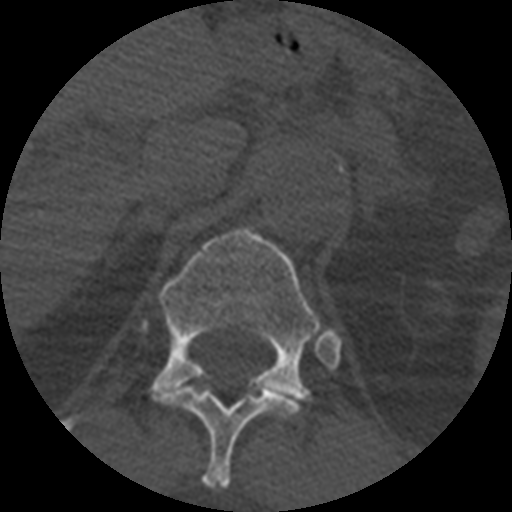
CT including the spine, one axial slice. Position 396 of 399 along the scan axis. Reconstruction kernel STANDARD. Bone window (W 1800 / L 400 HU). 1.25 mm slice thickness. 512 × 512 image matrix, field of view 160 × 160 mm. Patient age 71 years. Case-level facts recorded for this patient, not image findings: primary cancer: prostate.
Outlined on this slice (semi-automatically segmented with operator editing):
- T11 vertebra: bounding box (x1, y1, x2, y2) in pixels: (156, 386, 301, 489)
- T12 vertebra: (151, 227, 321, 408)